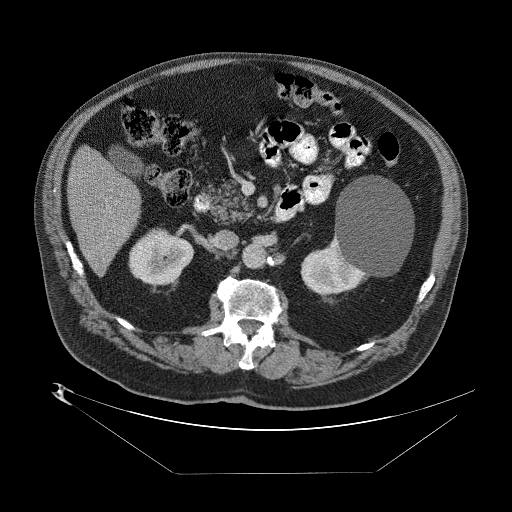
Contrast-enhanced abdominal CT (liver protocol), one axial slice. Position 23 of 89 along the scan axis. One of 2 acquisitions stored at this slice position. Soft-tissue window (W 400 / L 40 HU). 2.5 mm slice thickness. 512 × 512 image matrix, field of view 480 × 480 mm. Case-level facts recorded for this patient, not image findings: diagnosis: hepatocellular carcinoma (patient treated with transarterial chemoembolisation; whether this scan precedes or follows treatment is not stated here); TNM stage (as recorded): Stage-II; Child-Pugh class: B; tumour differentiation: moderately differentiated; tumour size: 4 cm.
Annotated regions visible in this slice (semi-automatic segmentation, software-assisted and operator-edited):
- abdominal aorta: bounding box <244,245,266,268> (left, top, right, bottom; pixels)
- liver parenchyma outside the tumour (the mass and vessels are separate outlines, so this box may not span the whole liver): <64,142,140,272>
- liver vessels: <105,204,125,238>